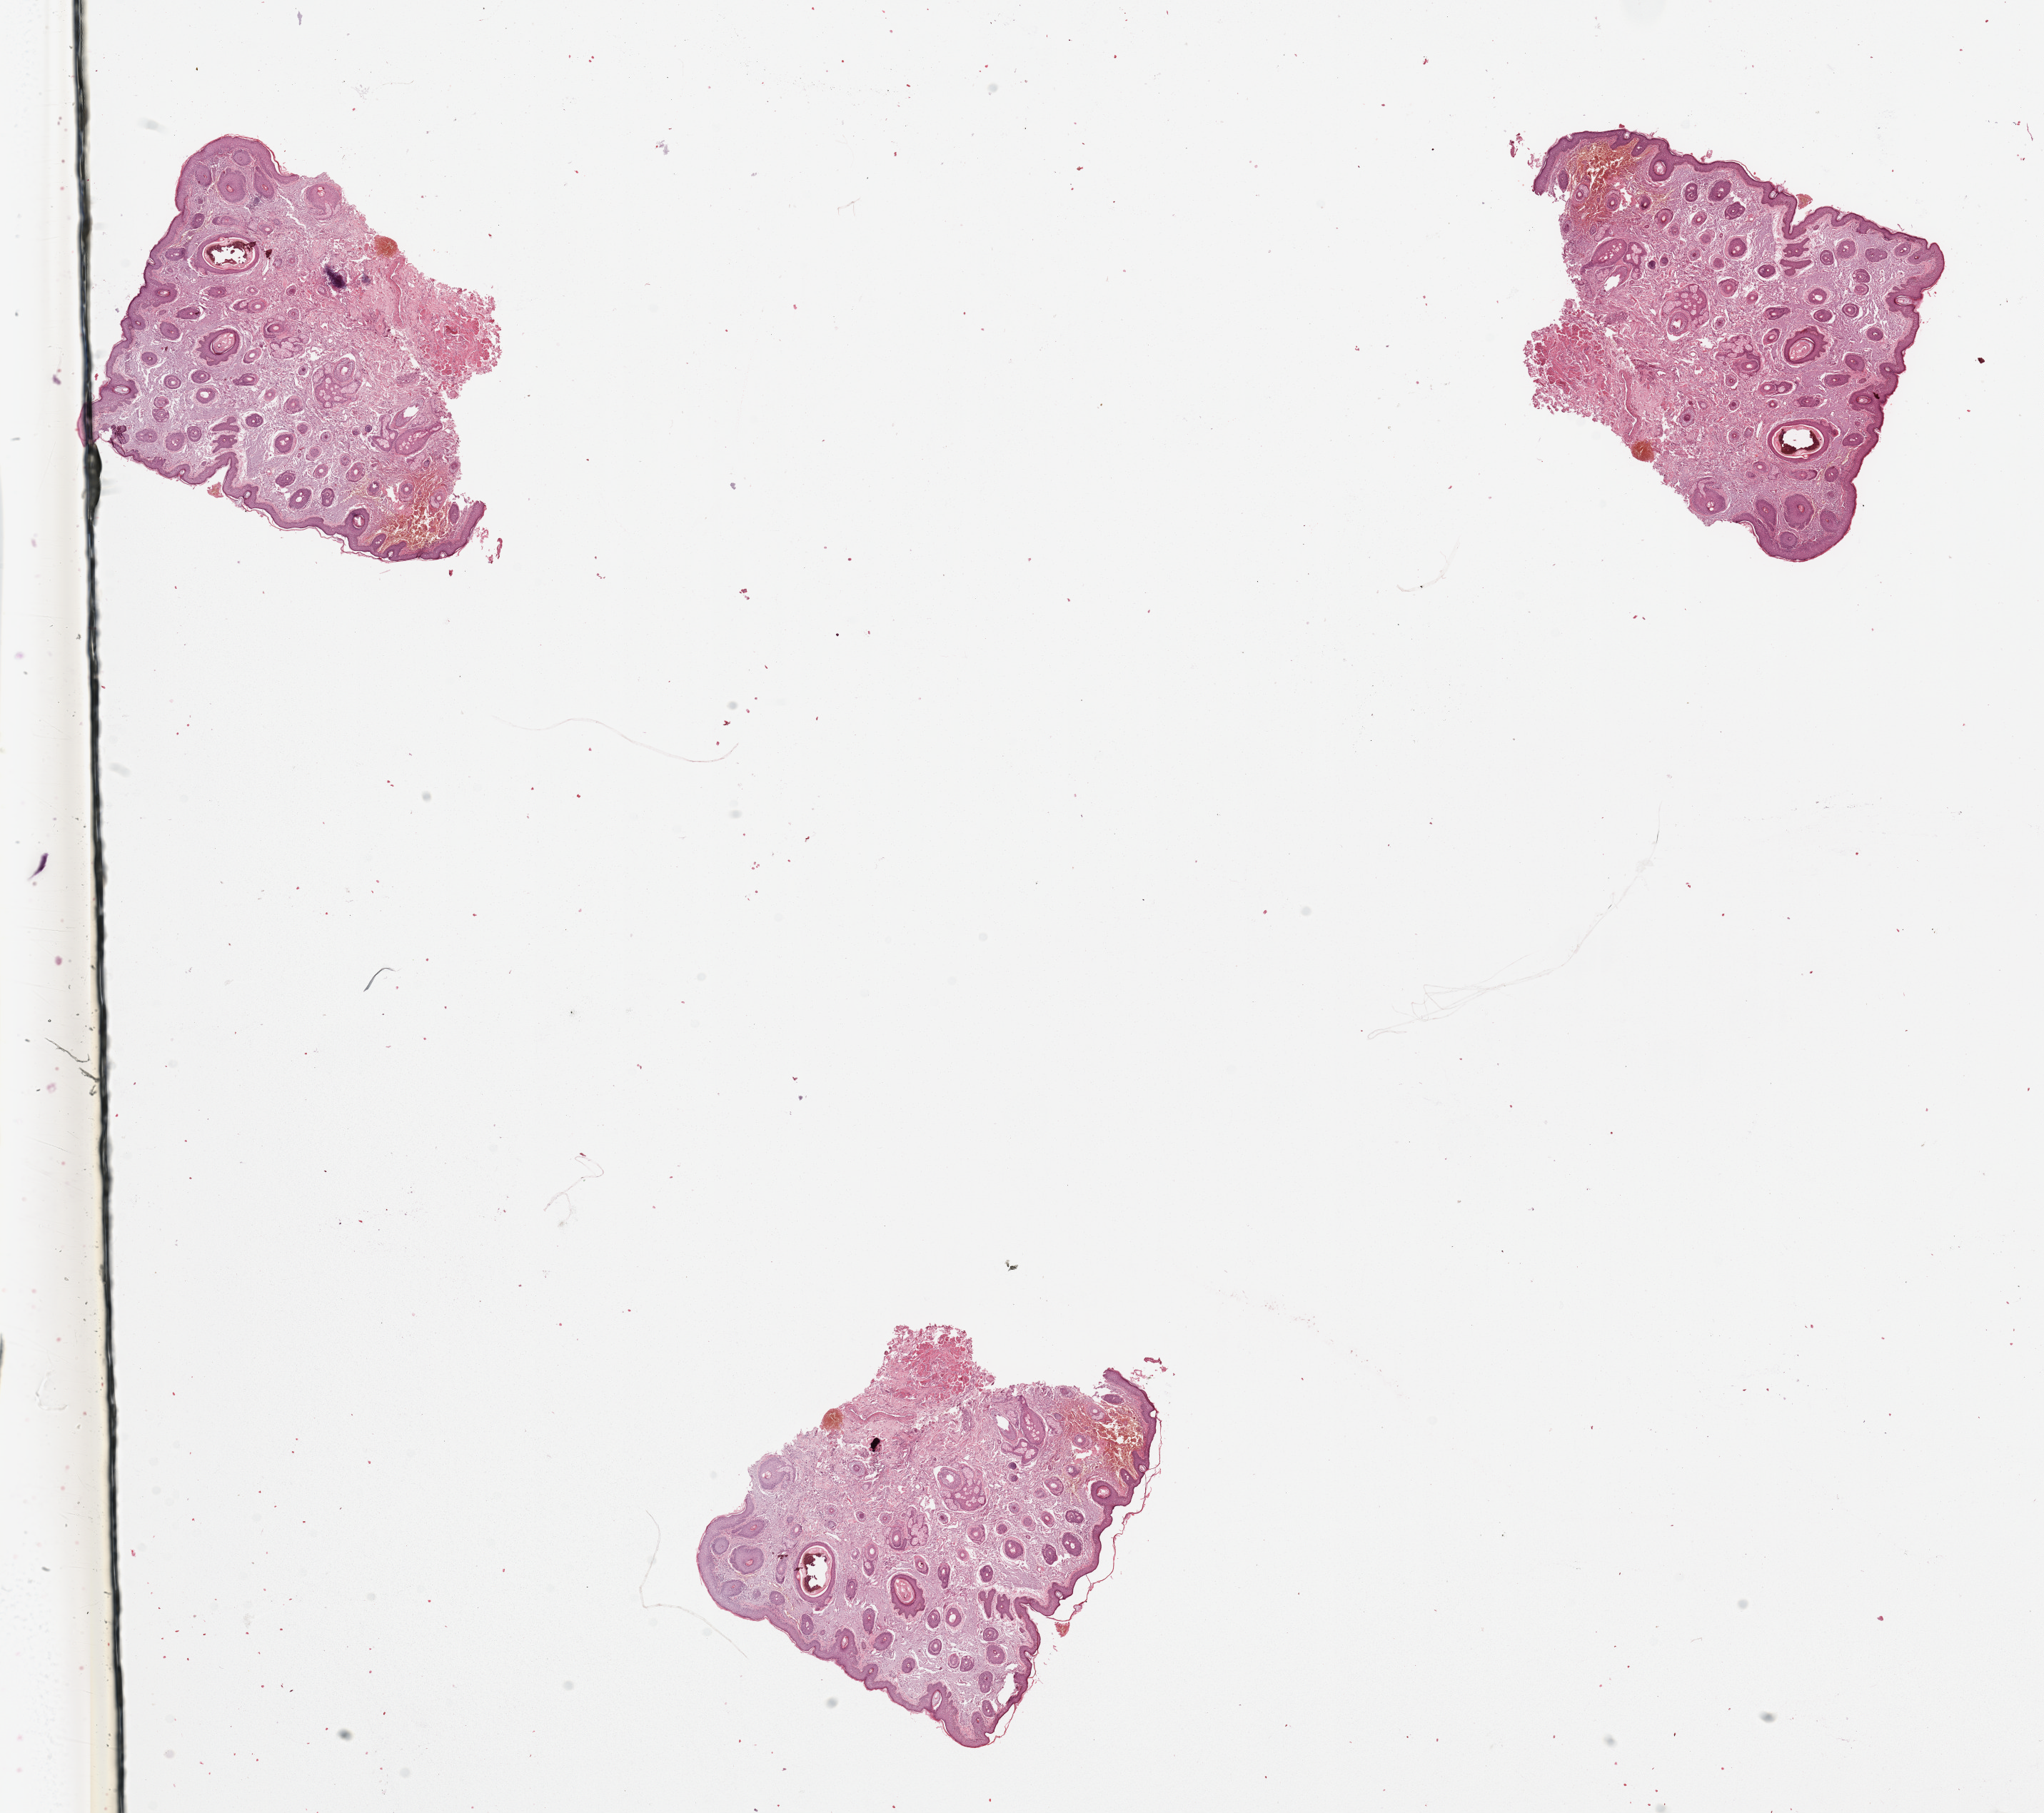
Whole-slide histology image, H&E-stained, low-resolution overview of the scanned area, about 22.6 x 20.1 mm (from a 20x scan); head and neck, tissue type not recorded. 80-year-old female patient.
Patient diagnosis: Squamous cell carcinoma, NOS (lip, NOS).